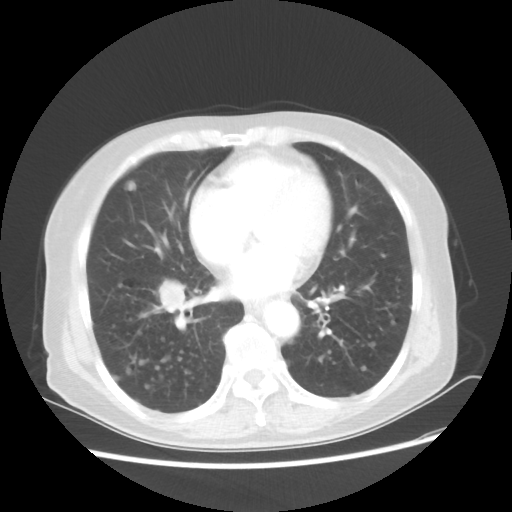
Chest CT, one axial slice; slice 23 of 56 in the series (ordered by position); 80 kVp; lung window (W 1500 / L -600 HU); 512 × 512 image matrix, field of view 360 × 360 mm. Female patient, age 68 years. From the clinical record (not read from this slice): clinical TNM (as recorded): T1c N3 M0.
Annotated regions visible in this slice (bounding box drawn by a radiologist):
- lung tumour (recorded histology: squamous cell carcinoma): box from (x=148, y=274) to (x=198, y=327) px